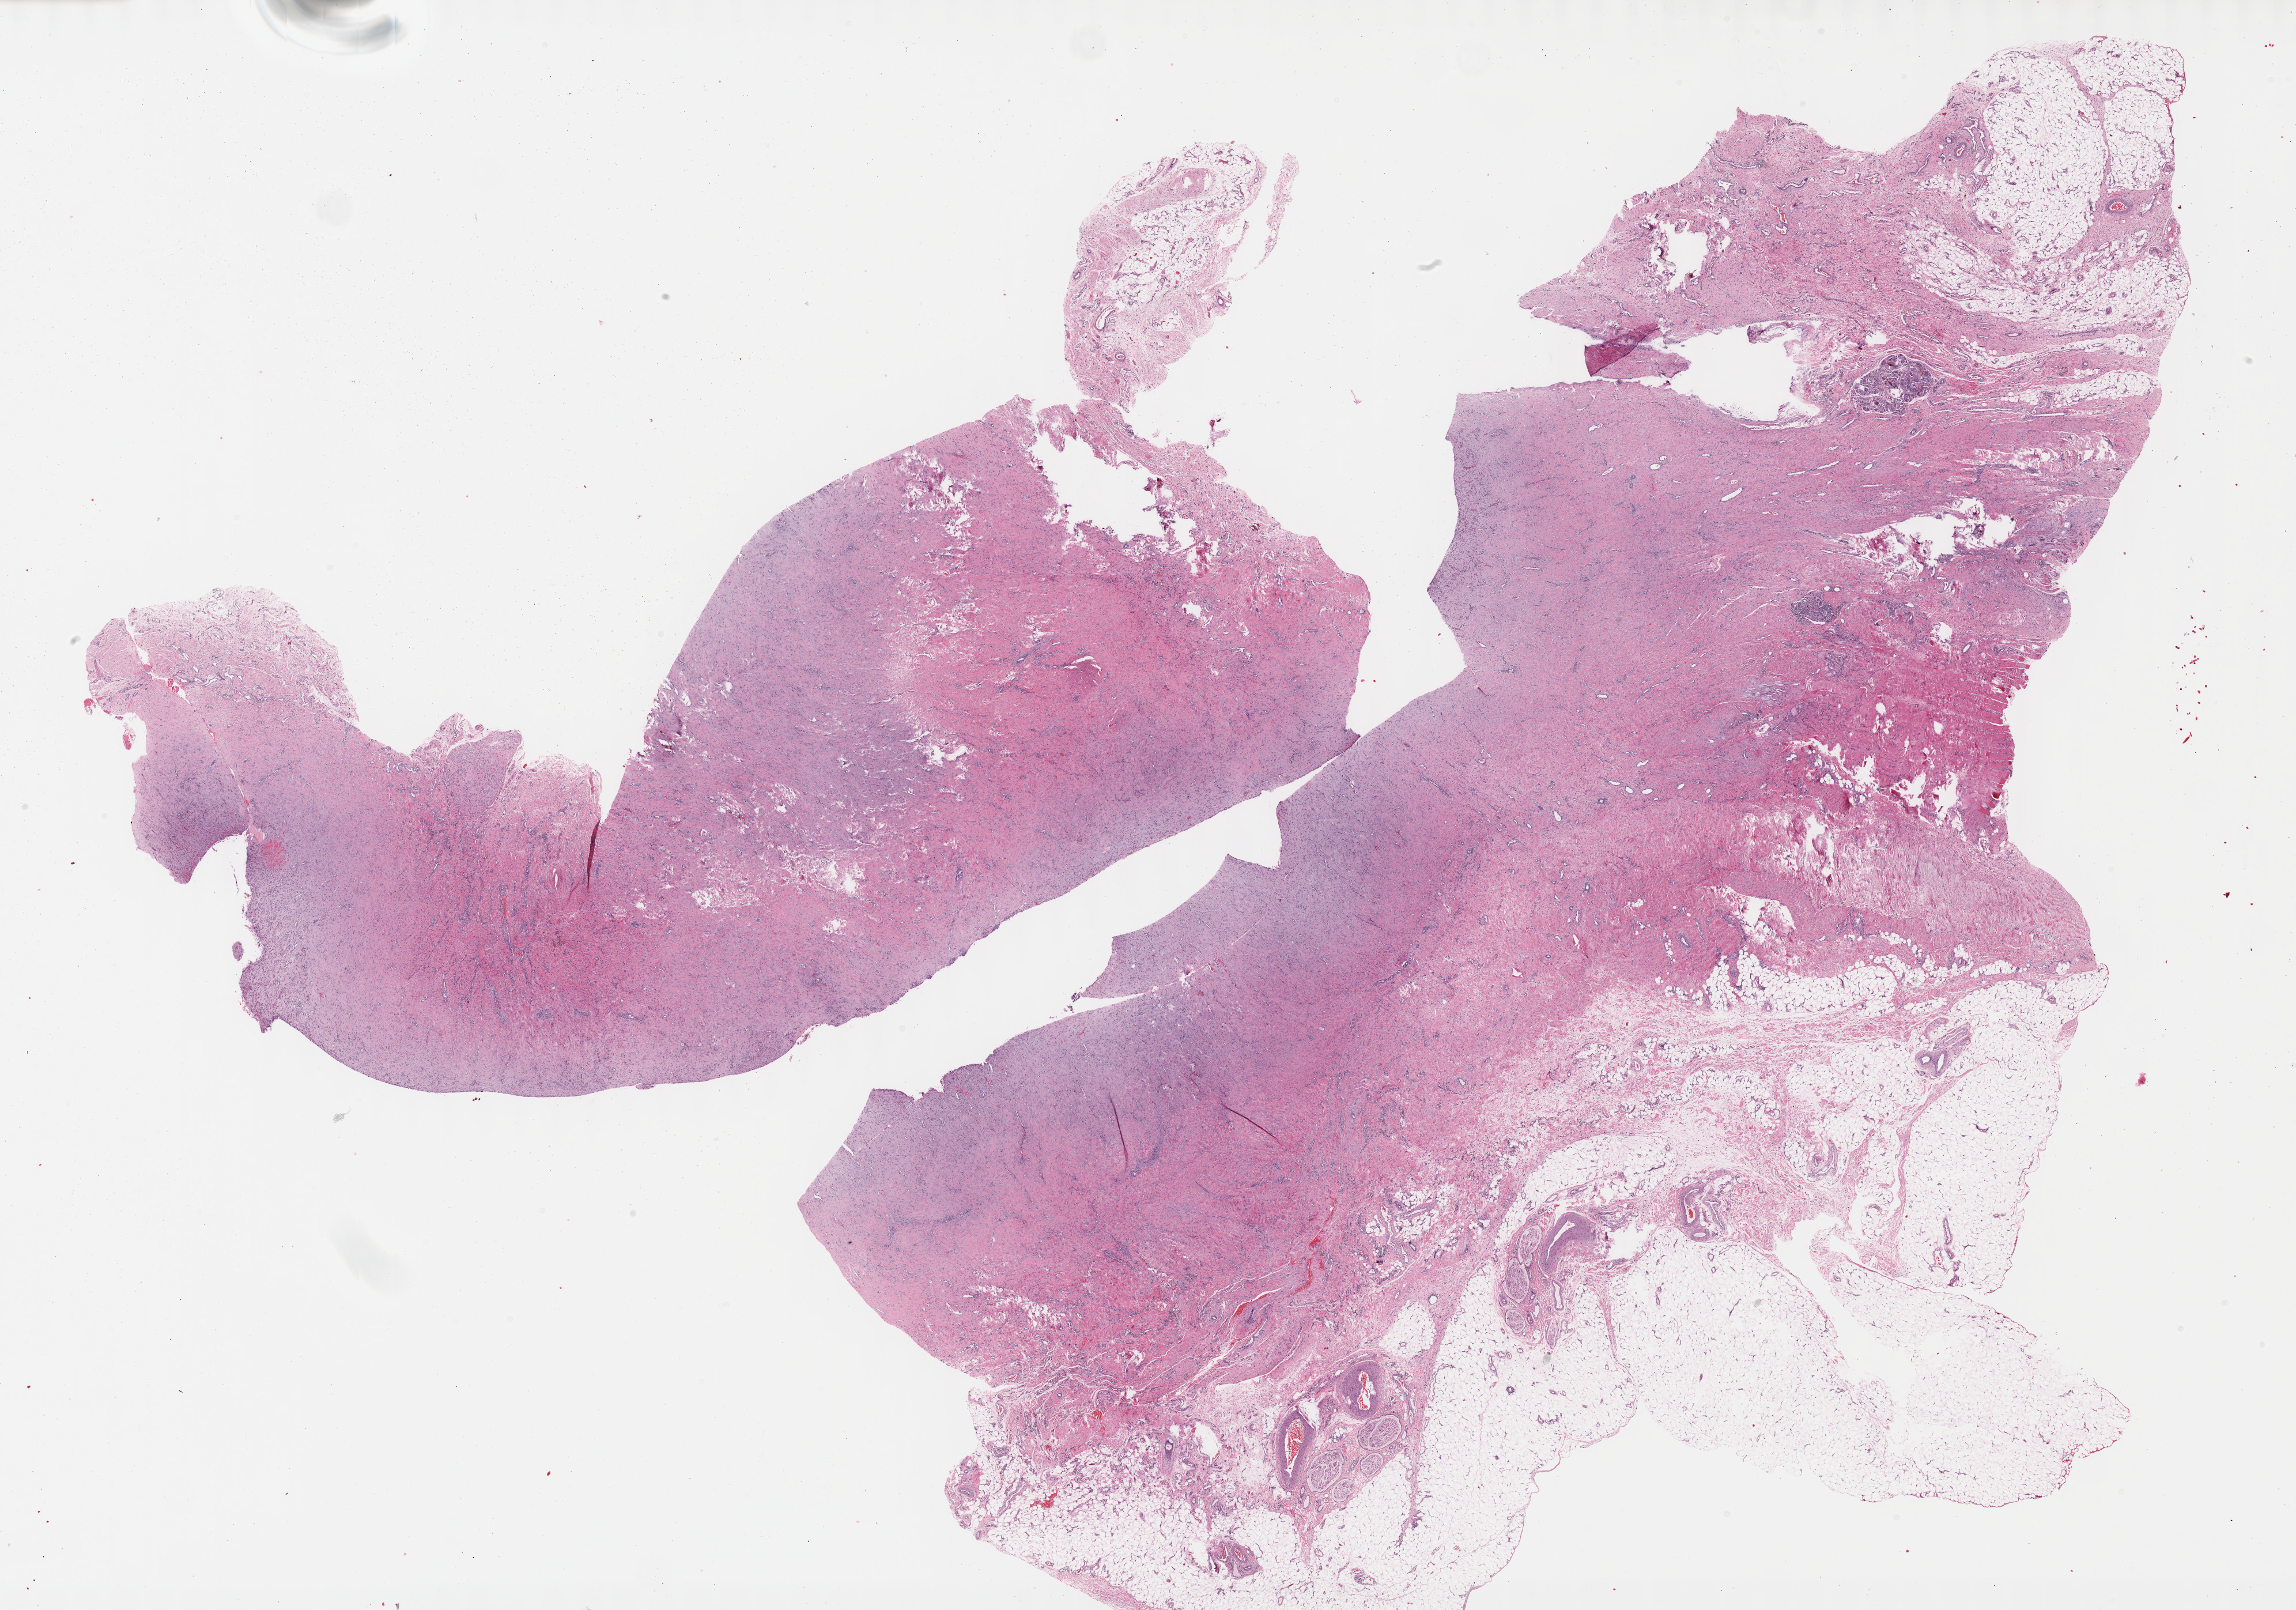
H&E whole-slide image, whole scanned area (about 32.2 x 22.6 mm) shown as a low-resolution overview; formalin-fixed paraffin-embedded (FFPE) diagnostic section; connective, subcutaneous and other soft tissues, primary tumour sample. Male, age 35 years at initial diagnosis.
• pathologic diagnosis: Fibromyxosarcoma (connective, subcutaneous and other soft tissues of lower limb and hip)